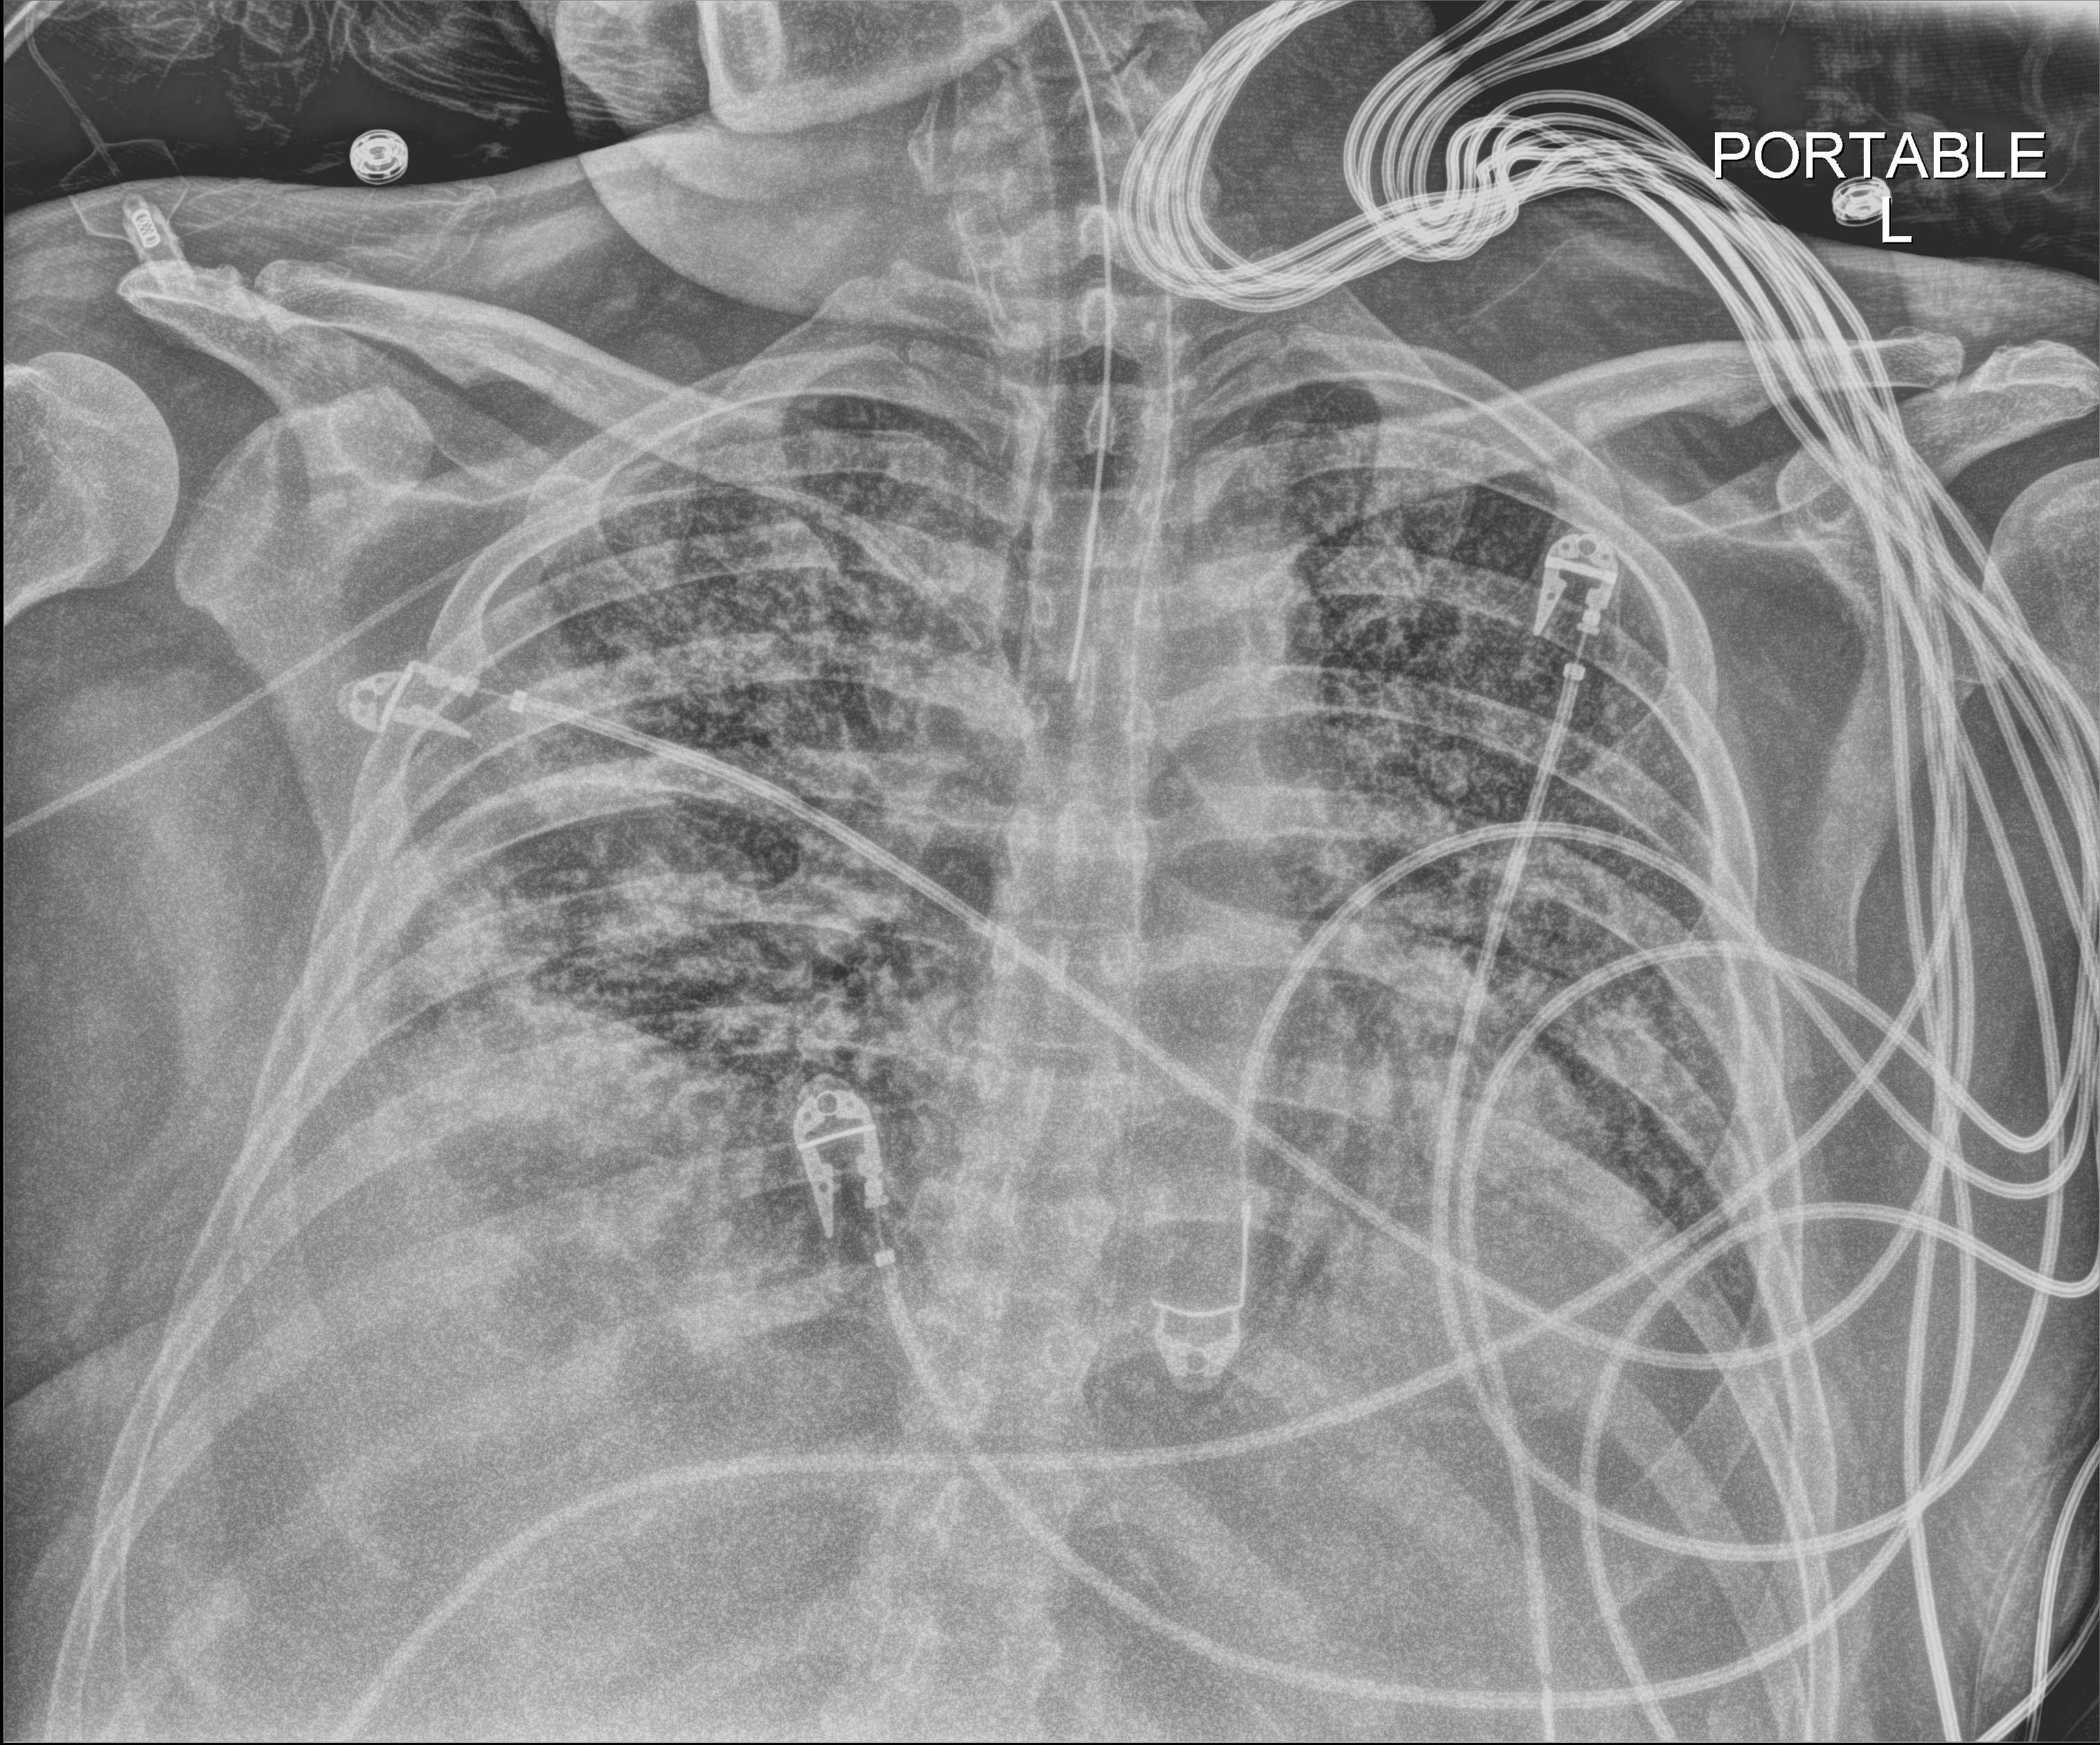
Bedside chest radiograph (digital radiography); anteroposterior (AP) projection. Male patient hospitalised with COVID-19, age 18–59 years.
Admission-level facts for this patient (not findings on this image; timing relative to this image not recorded): COPD (admission record): no.